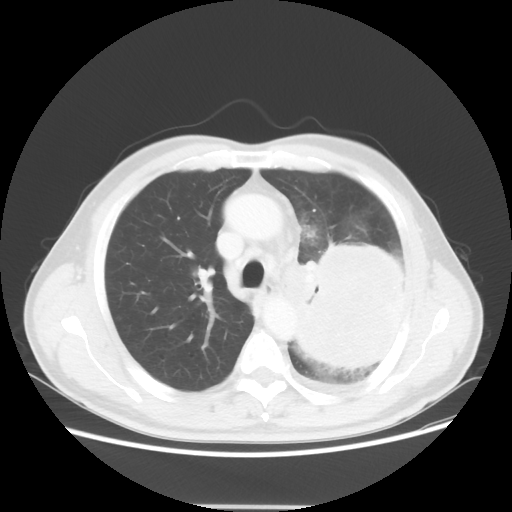
Chest CT, one axial slice. Position 37 of 53 along the scan axis. Lung window (W 1500 / L -600 HU). 5 mm slice thickness. 512 × 512 image matrix, field of view 391 × 391 mm. Male patient, age 60 years. Case-level facts recorded for this patient, not image findings: clinical TNM (as recorded): T4 N1 M1a.
Outlined on this slice (bounding box drawn by a radiologist):
- lung tumour (recorded histology: large cell carcinoma): box from (x=301, y=242) to (x=406, y=384) px